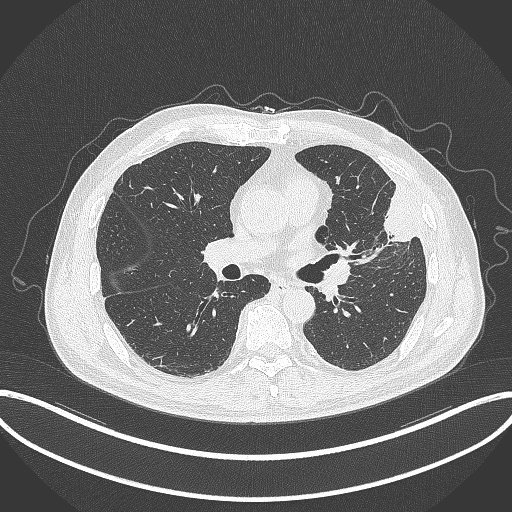
Chest CT, one axial slice; reconstruction kernel B70f; 120 kVp; lung window (W 1500 / L -600 HU); 1 mm slice thickness; 512 × 512 image matrix, field of view 415 × 415 mm. Male patient, age 64 years. From the clinical record (not read from this slice): clinical TNM (as recorded): T4 N1 M0.
Structures marked on this image (bounding box drawn by a radiologist):
- lung tumour (recorded histology: adenocarcinoma): bounding box (x1, y1, x2, y2) in pixels: (365, 184, 419, 250)